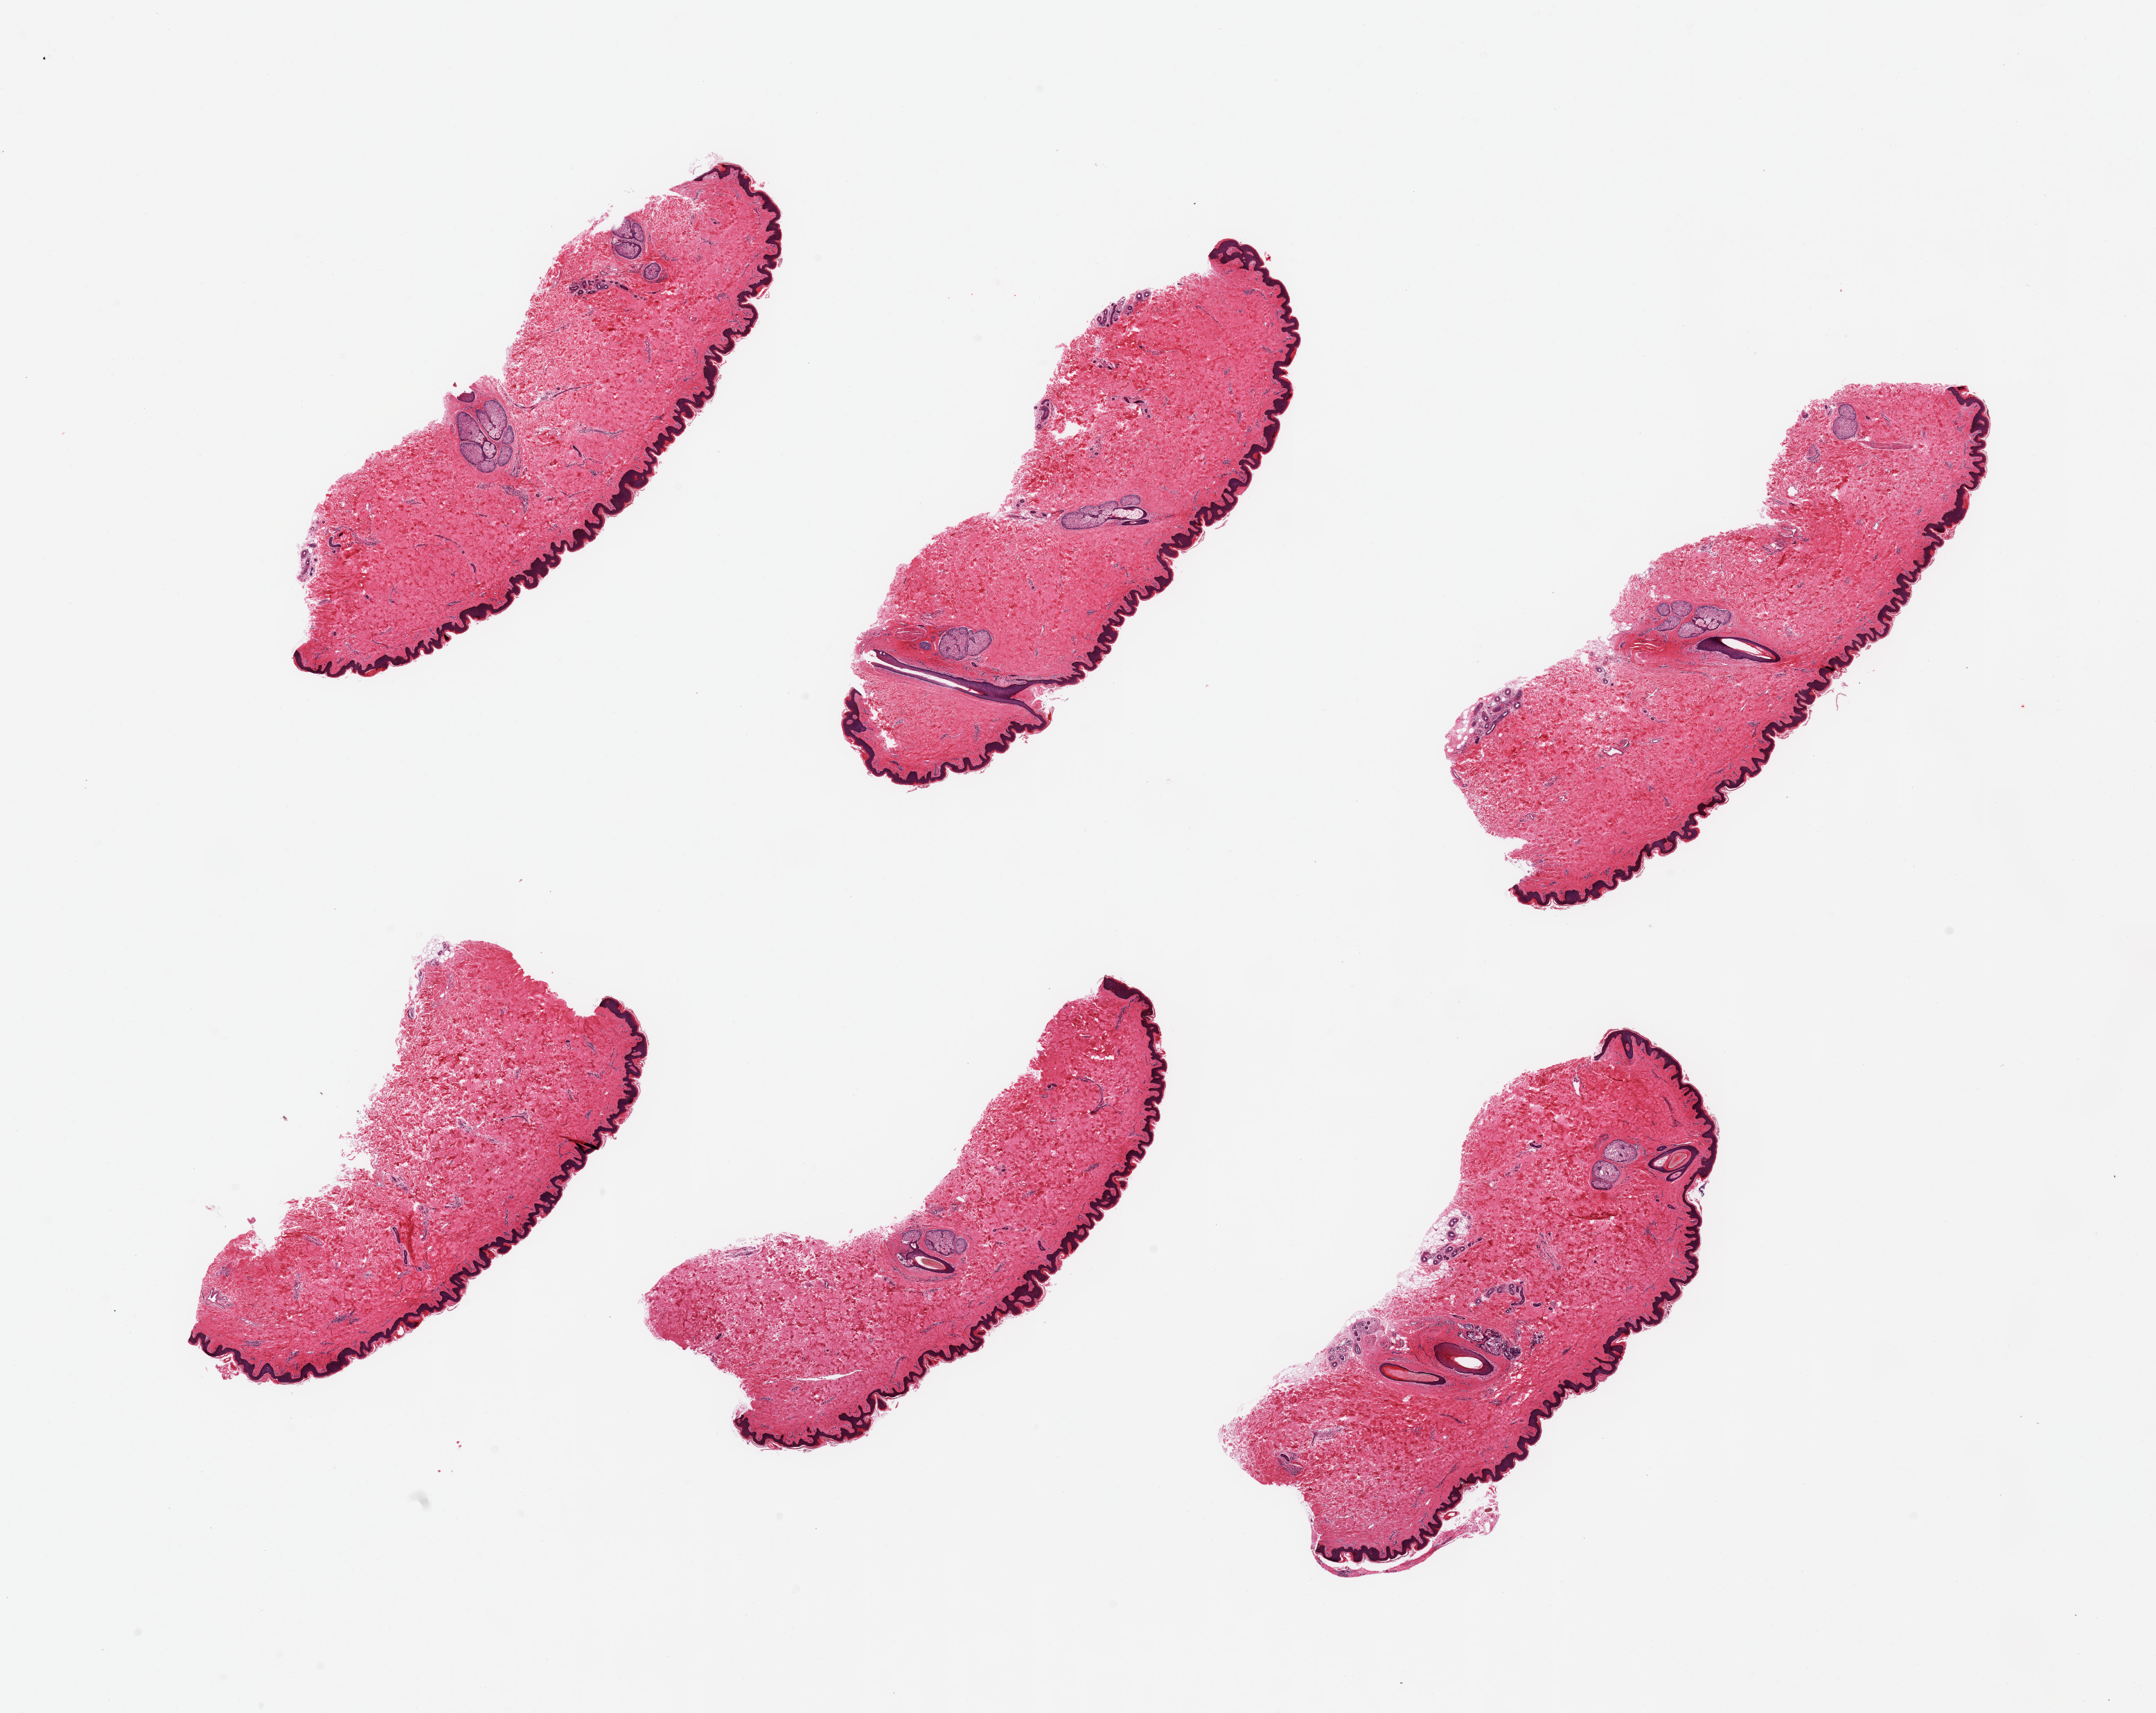
Whole-slide image, hematoxylin and eosin (H&E) stain — whole scanned area (about 24.6 x 19.5 mm) shown as a low-resolution overview; PAXgene-fixed paraffin-embedded (PFPE) section; section of skin of suprapubic region (target tissue); tissue donor sample. Donor: female.
Reviewer comment on this tissue sample: 6 pieces; well trimmed hair bearing skin.